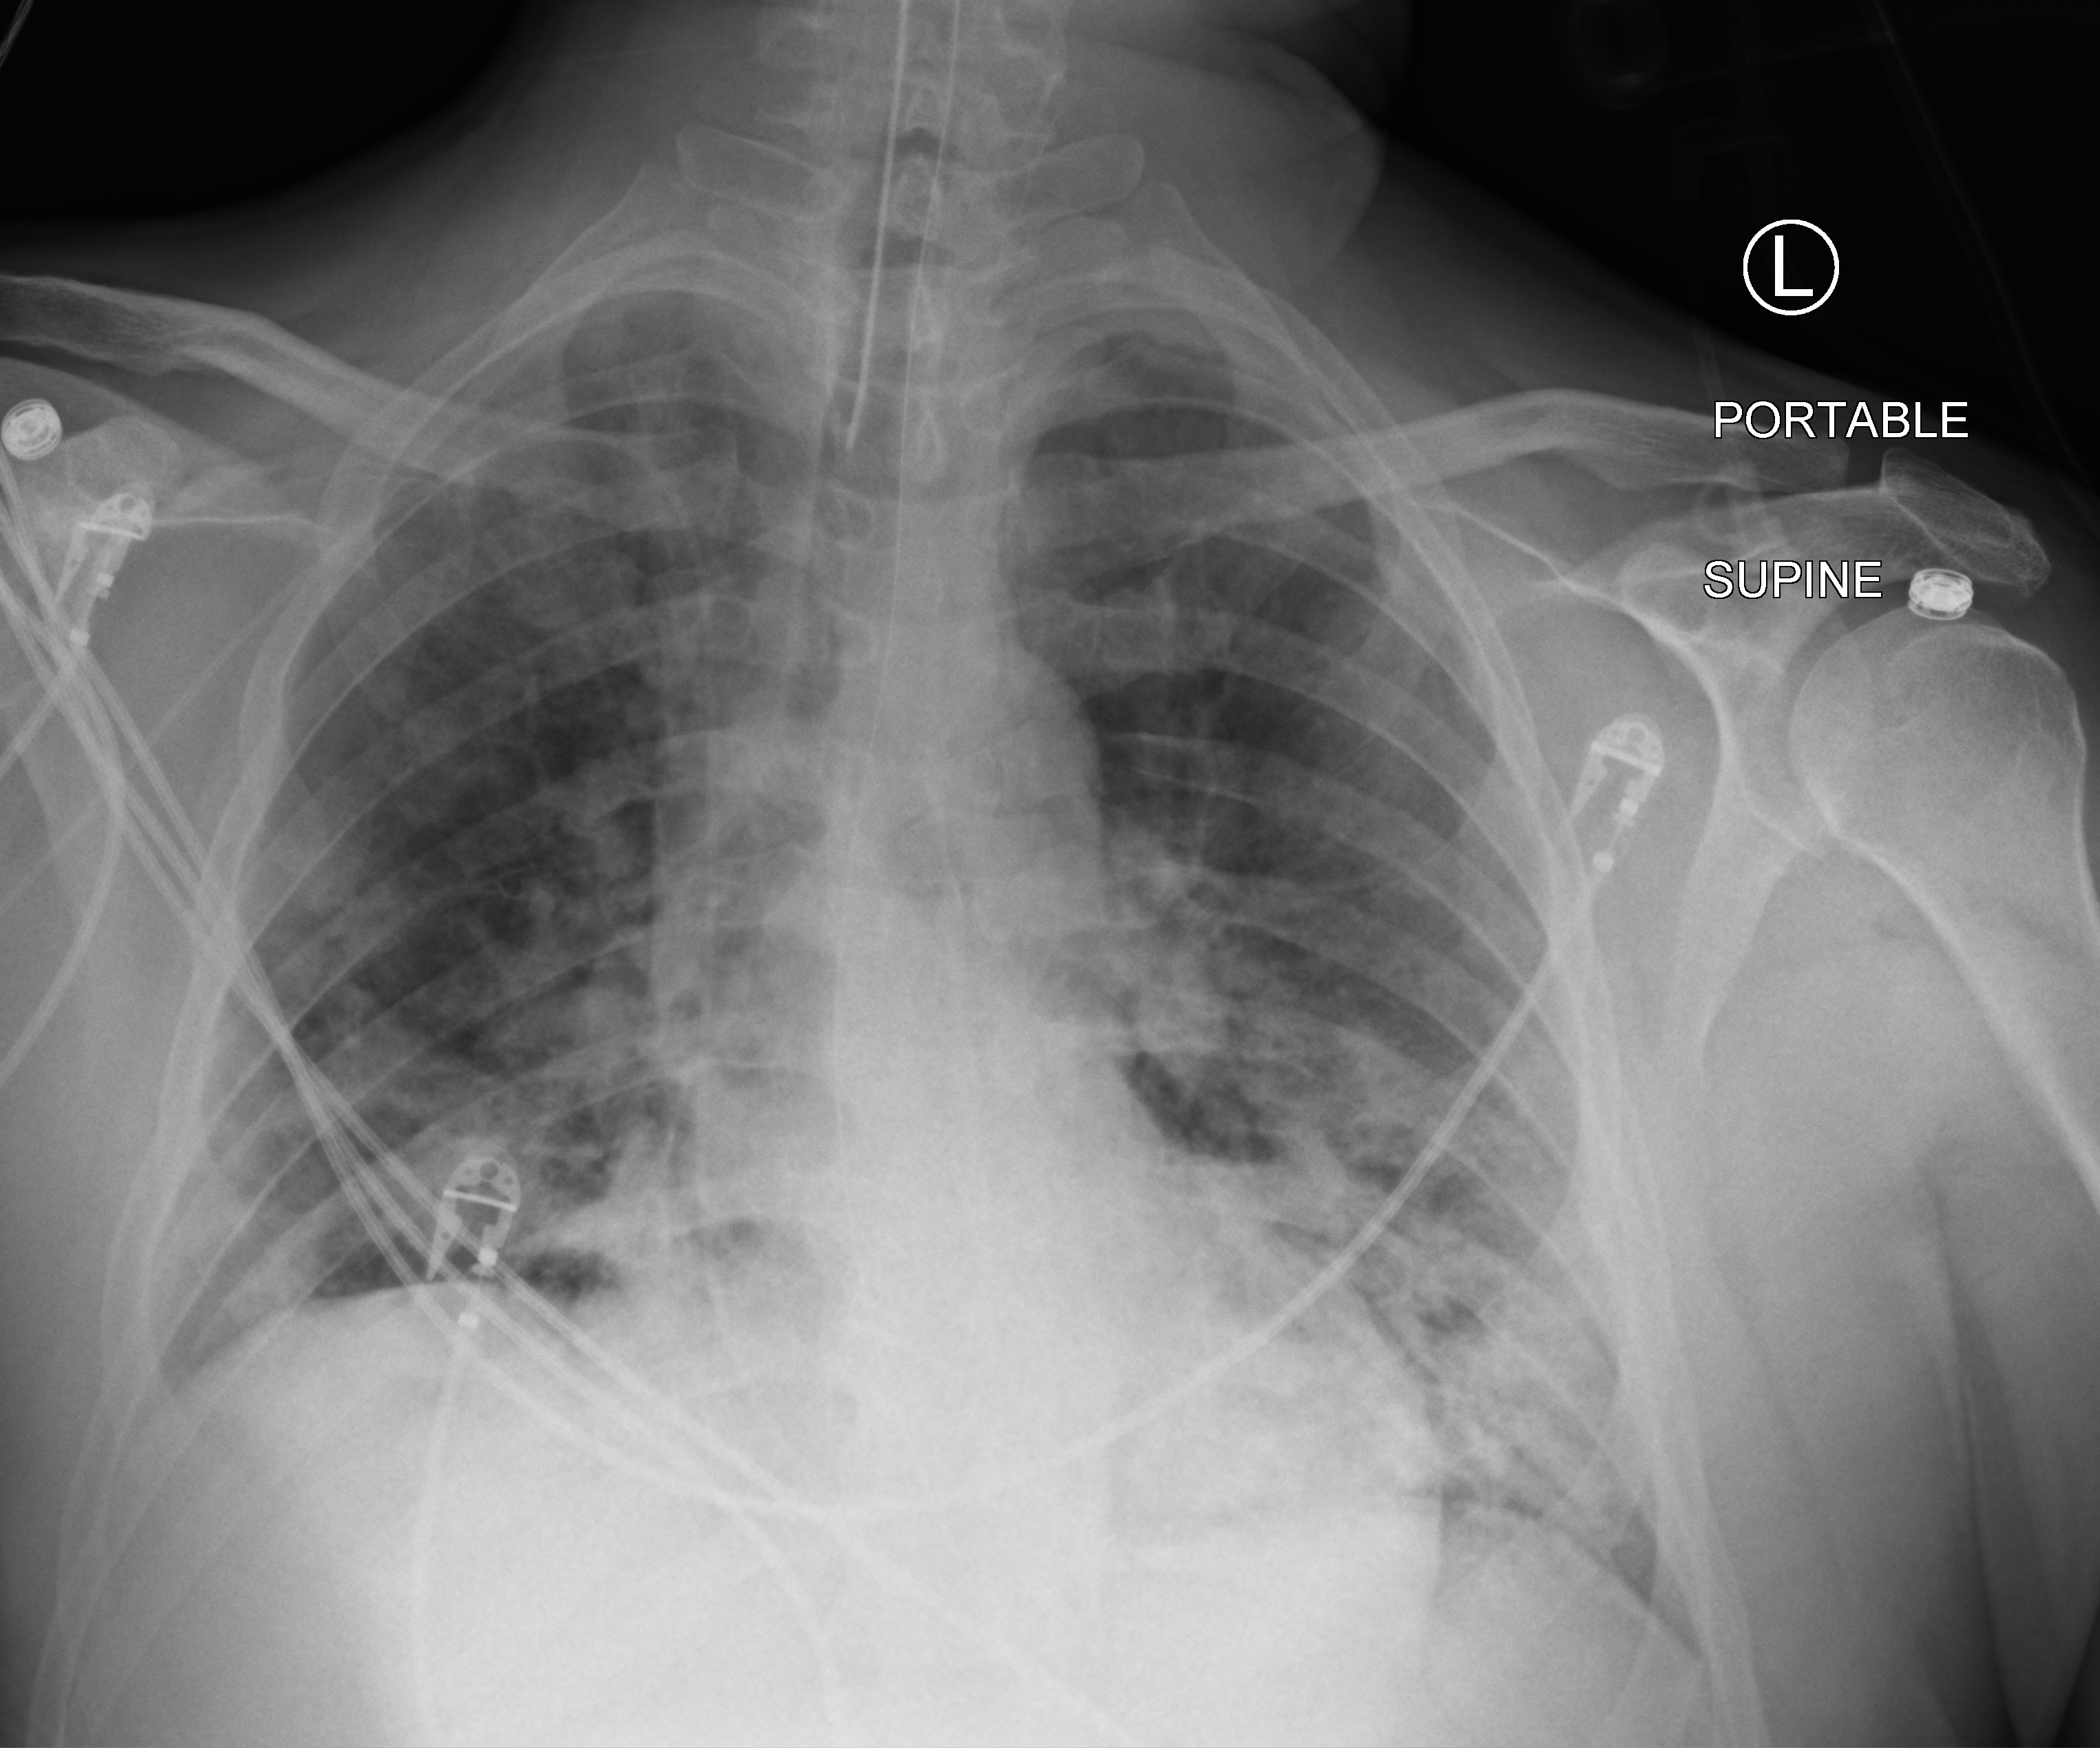
Chest X-ray (portable). Patient hospitalised with COVID-19; male, aged 18–59 years.
From the hospital-stay record, not from the radiograph (when in the stay this image was taken is not recorded):
- mechanically ventilated during this hospital stay: yes